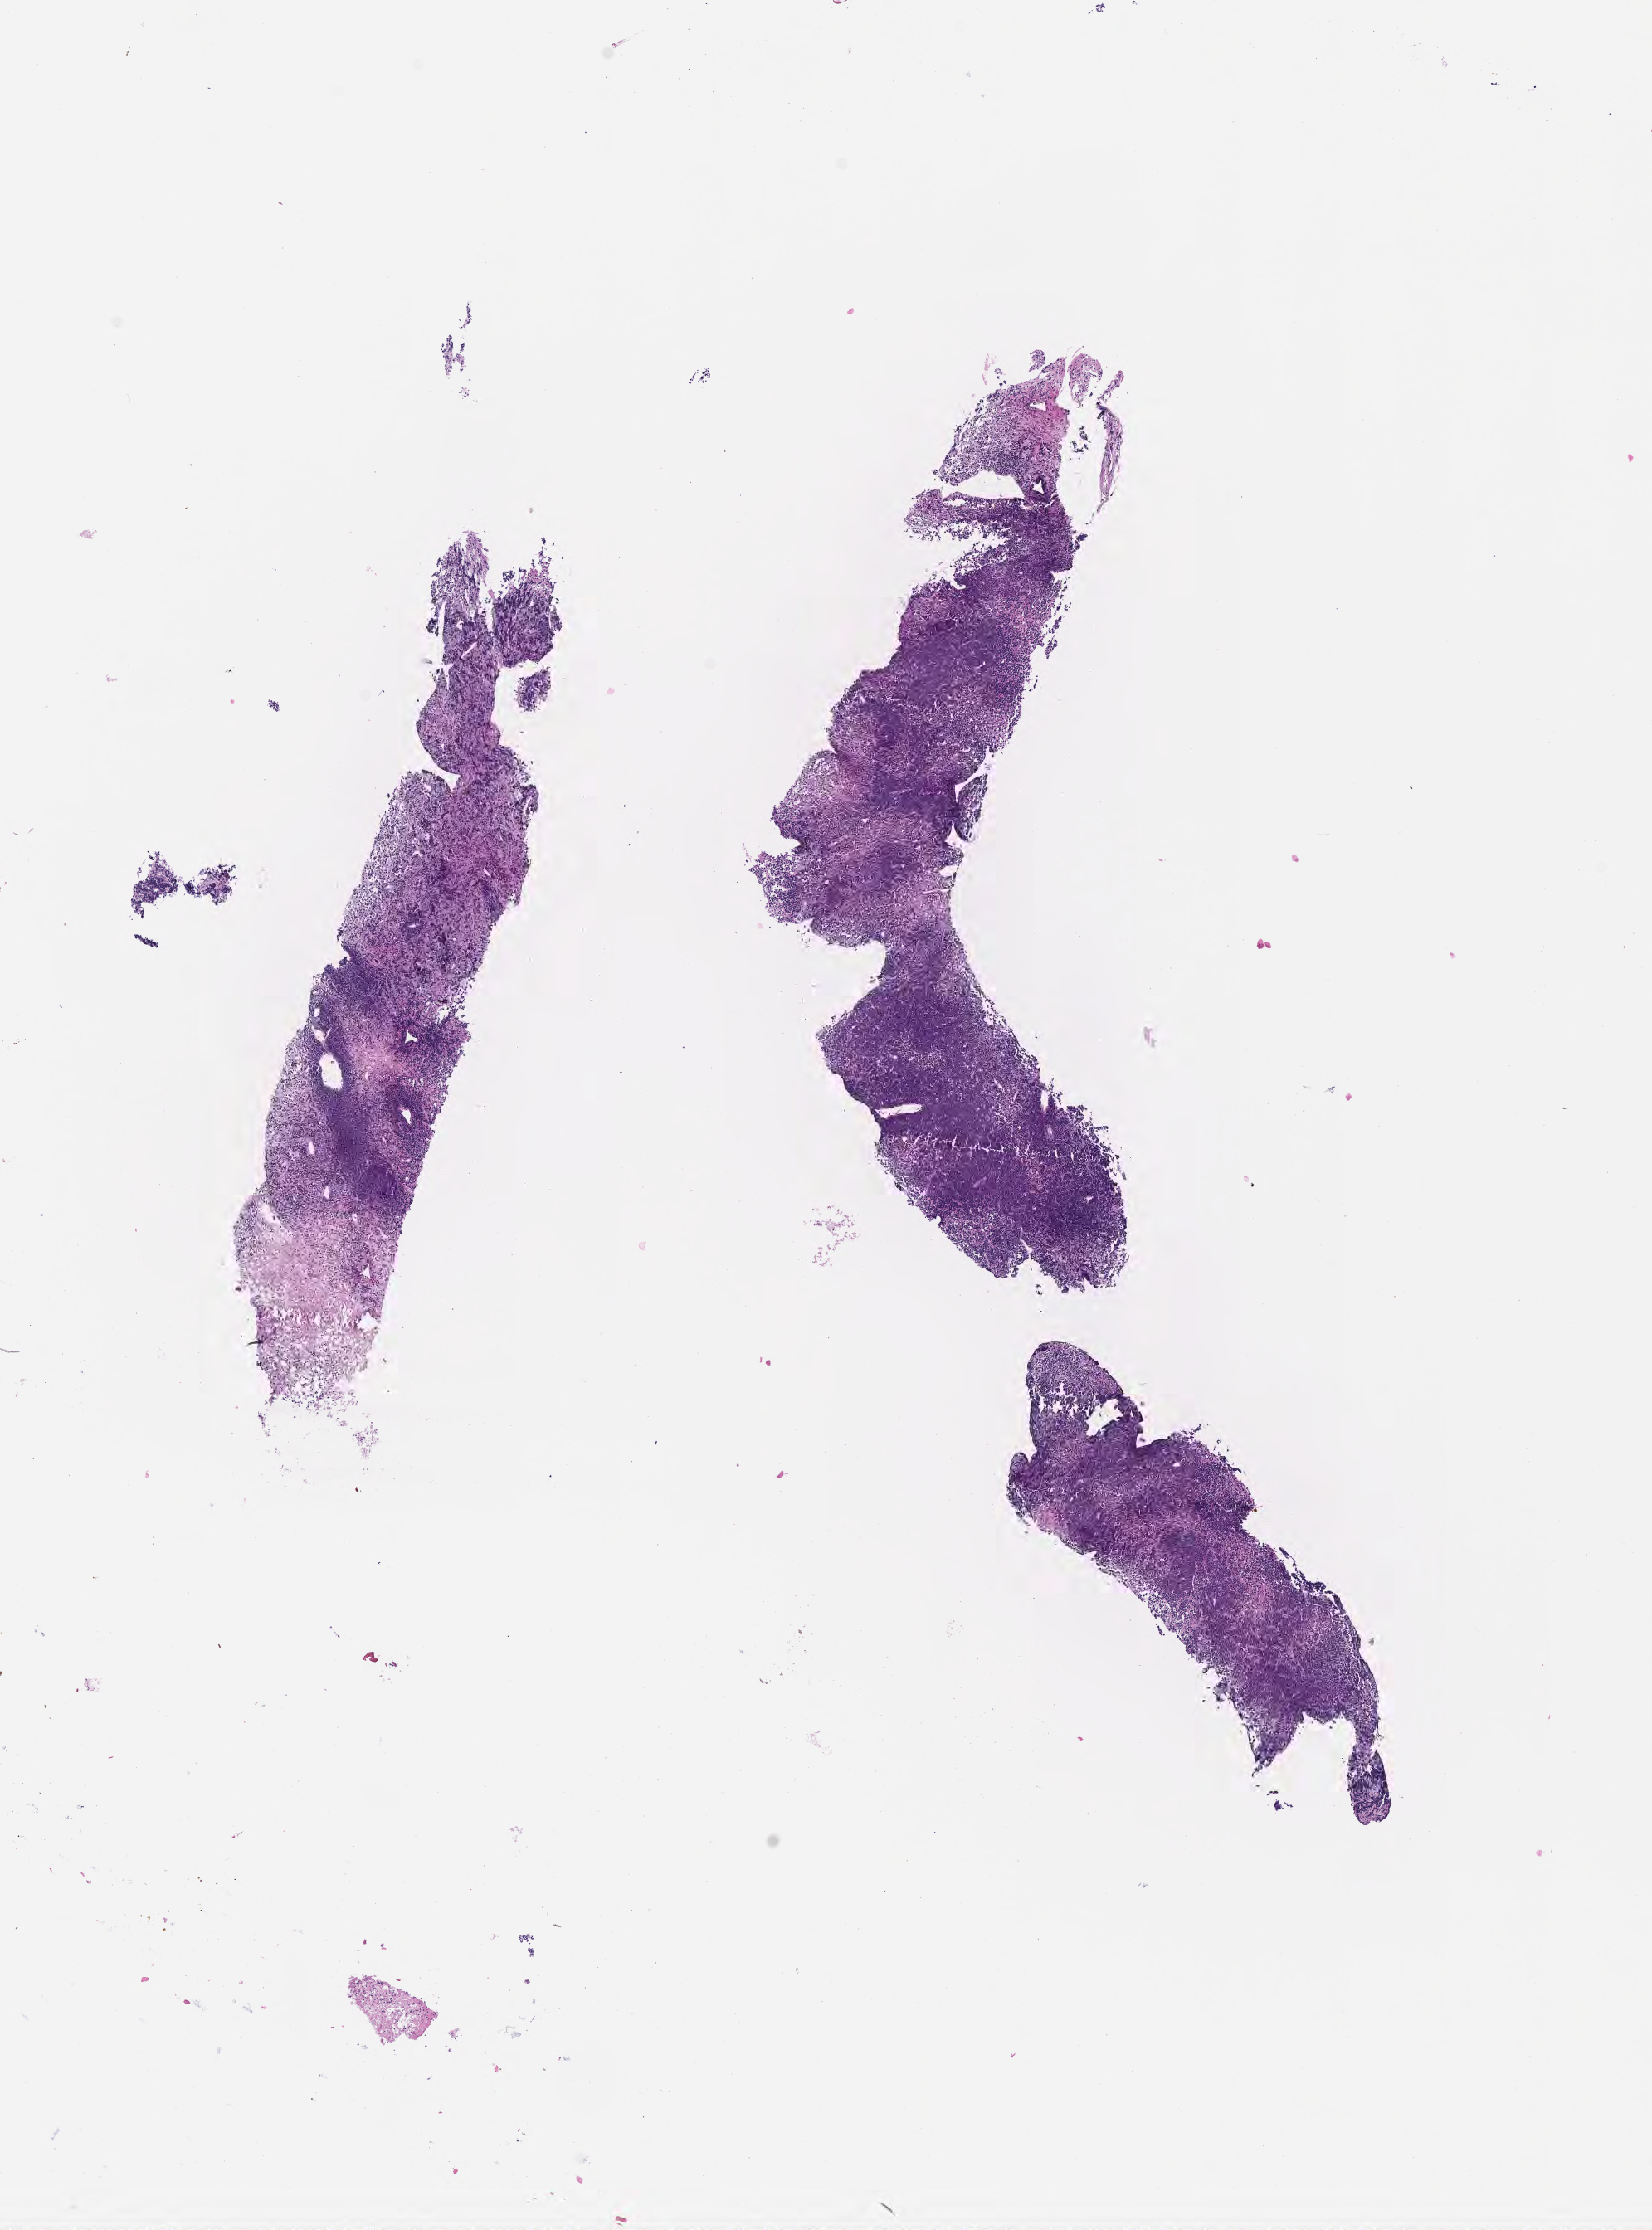
Digitized H&E-stained section, shown as a low-resolution overview of the whole scanned area (about 8.1 x 10.9 mm). Specimen: tumor tissue. Patient female; 12 years old.
Diagnosis: Burkitt lymphoma, NOS.